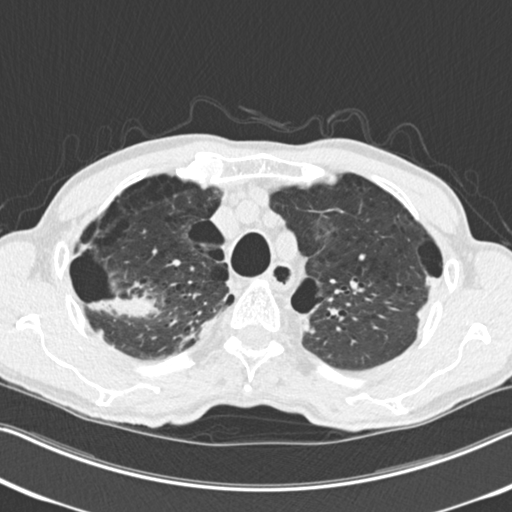
Low-dose screening chest CT, one axial slice. Reconstruction kernel B30f. Lung window (W 1500 / L -600 HU). 512 × 512 image matrix.
Outlined on this slice (outlined manually by an expert reader):
- lesion 1 (tumor, upper lobe of right lung): box from (x=87, y=294) to (x=156, y=318) px